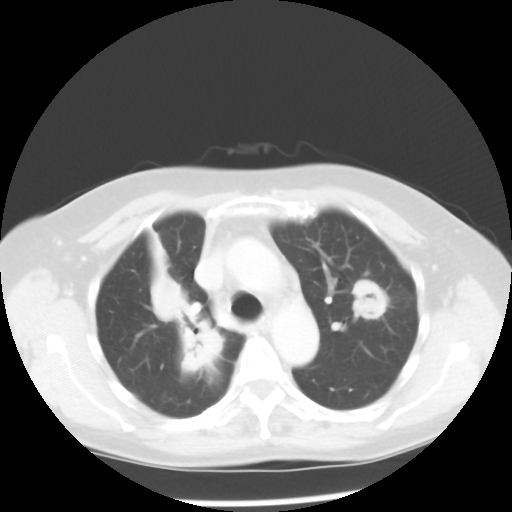
Chest CT, one axial slice; position 36 of 52 along the scan axis; reconstruction kernel STANDARD; 100 kVp; lung window (W 1500 / L -600 HU); 5 mm slice thickness; 512 × 512 image matrix. Female patient, age 60 years. From the clinical record (not read from this slice): clinical TNM (as recorded): T2 N1 M1a.
Structures marked on this image (rectangle marked by the reading radiologist):
- lung tumour (recorded histology: adenocarcinoma): box from (x=149, y=268) to (x=222, y=375) px